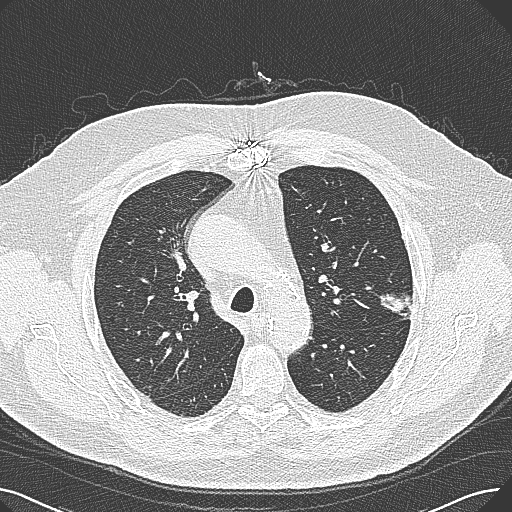
Axial slice from a low-dose chest CT screening exam. Baseline screening round. Lung window (W 1500 / L -600 HU). Slice 86 of 269 in the series. Male participant, aged 74 years at enrolment. Former smoker at enrolment.
Expert reader's lesion annotation, bounding box [x1, y1, x2, y2] px = [370, 273, 426, 322]. The exam's reader record, not a measurement of the box and not confirmed to be the same lesion: non-calcified nodule or mass ≥4 mm, left upper lobe, 15 × 10 mm, poorly defined margins, soft tissue attenuation.